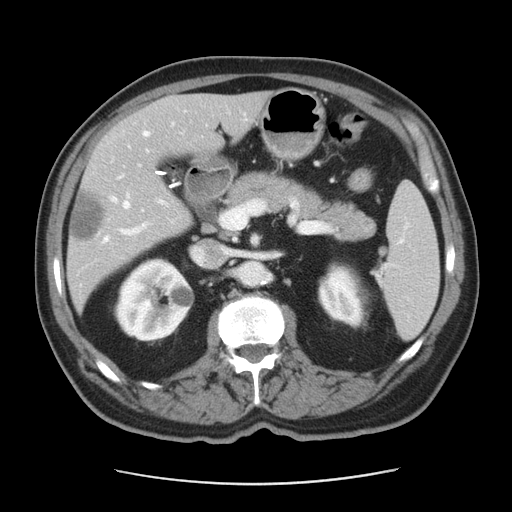
Contrast-enhanced abdominal CT, one axial slice. Slice 23 of 42 in the series (ordered by position). Reconstruction kernel STANDARD. 120 kVp. Intravenous contrast given. Soft-tissue window (W 400 / L 40 HU). 5 mm slice thickness. 512 × 512 image matrix, field of view 370 × 370 mm. Male patient, age 73 years. Case-level facts recorded for this patient, not image findings: diagnosis: colorectal cancer liver metastases, imaged before liver resection; multiple liver metastases: yes; largest metastasis: 0.5 cm; disease in both lobes: no.
Structures marked on this image (outlined manually by an expert reader):
- hepatic veins: bounding box (x1, y1, x2, y2) in pixels: (102, 132, 149, 244)
- liver: (68, 92, 268, 306)
- planned liver remnant (the part of the liver to remain after resection): (110, 92, 268, 172)
- portal vein (with intrahepatic branches): (121, 217, 222, 235)
- liver metastasis: (72, 192, 106, 241)